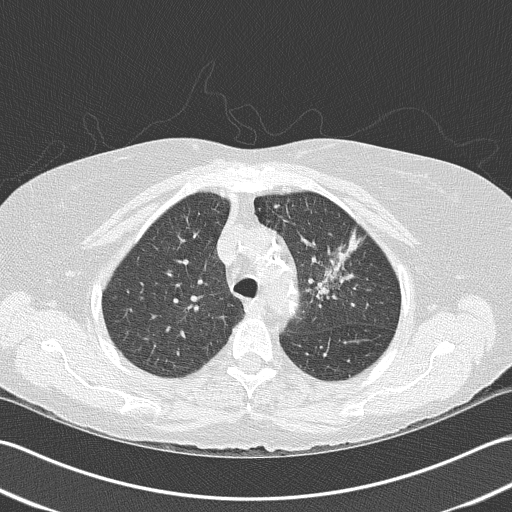
Chest CT (low-dose screening protocol), one axial image; baseline screening round; lung window (W 1500 / L -600 HU); 2 mm slice thickness; slice 121 of 159 in the series. Female participant, aged 68 years at enrolment. Former smoker at enrolment.
Lesion marked by an expert reader, bounding box <296,224,370,309> (left, top, right, bottom; pixels). No non-calcified nodule or mass ≥4 mm was recorded by the screening reader at this exam. Official screen result: negative screen, minor abnormalities not suspicious for lung cancer. Later outcome: lung cancer diagnosed 763 days after this screen (after the third annual screen) — adenocarcinoma, NOS, left upper lobe, poorly differentiated (G3), stage IB (AJCC 6th edition), 50 mm at pathology.